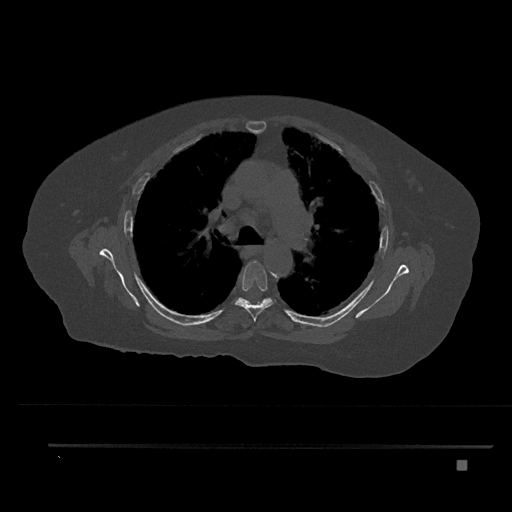
CT including the spine, one axial slice. 120 kVp. Bone window (W 1800 / L 400 HU). 0.5 mm slice thickness. 512 × 512 image matrix. Female patient, age 76 years. From the clinical record (not read from this slice): primary cancer: lung; vertebrae with lytic lesions (as recorded): T11, L3.
Outlined on this slice (semi-automatic segmentation, software-assisted and operator-edited):
- T5 vertebra: box from (x=235, y=261) to (x=274, y=322) px
- T6 vertebra: (x=236, y=298)–(x=273, y=305)